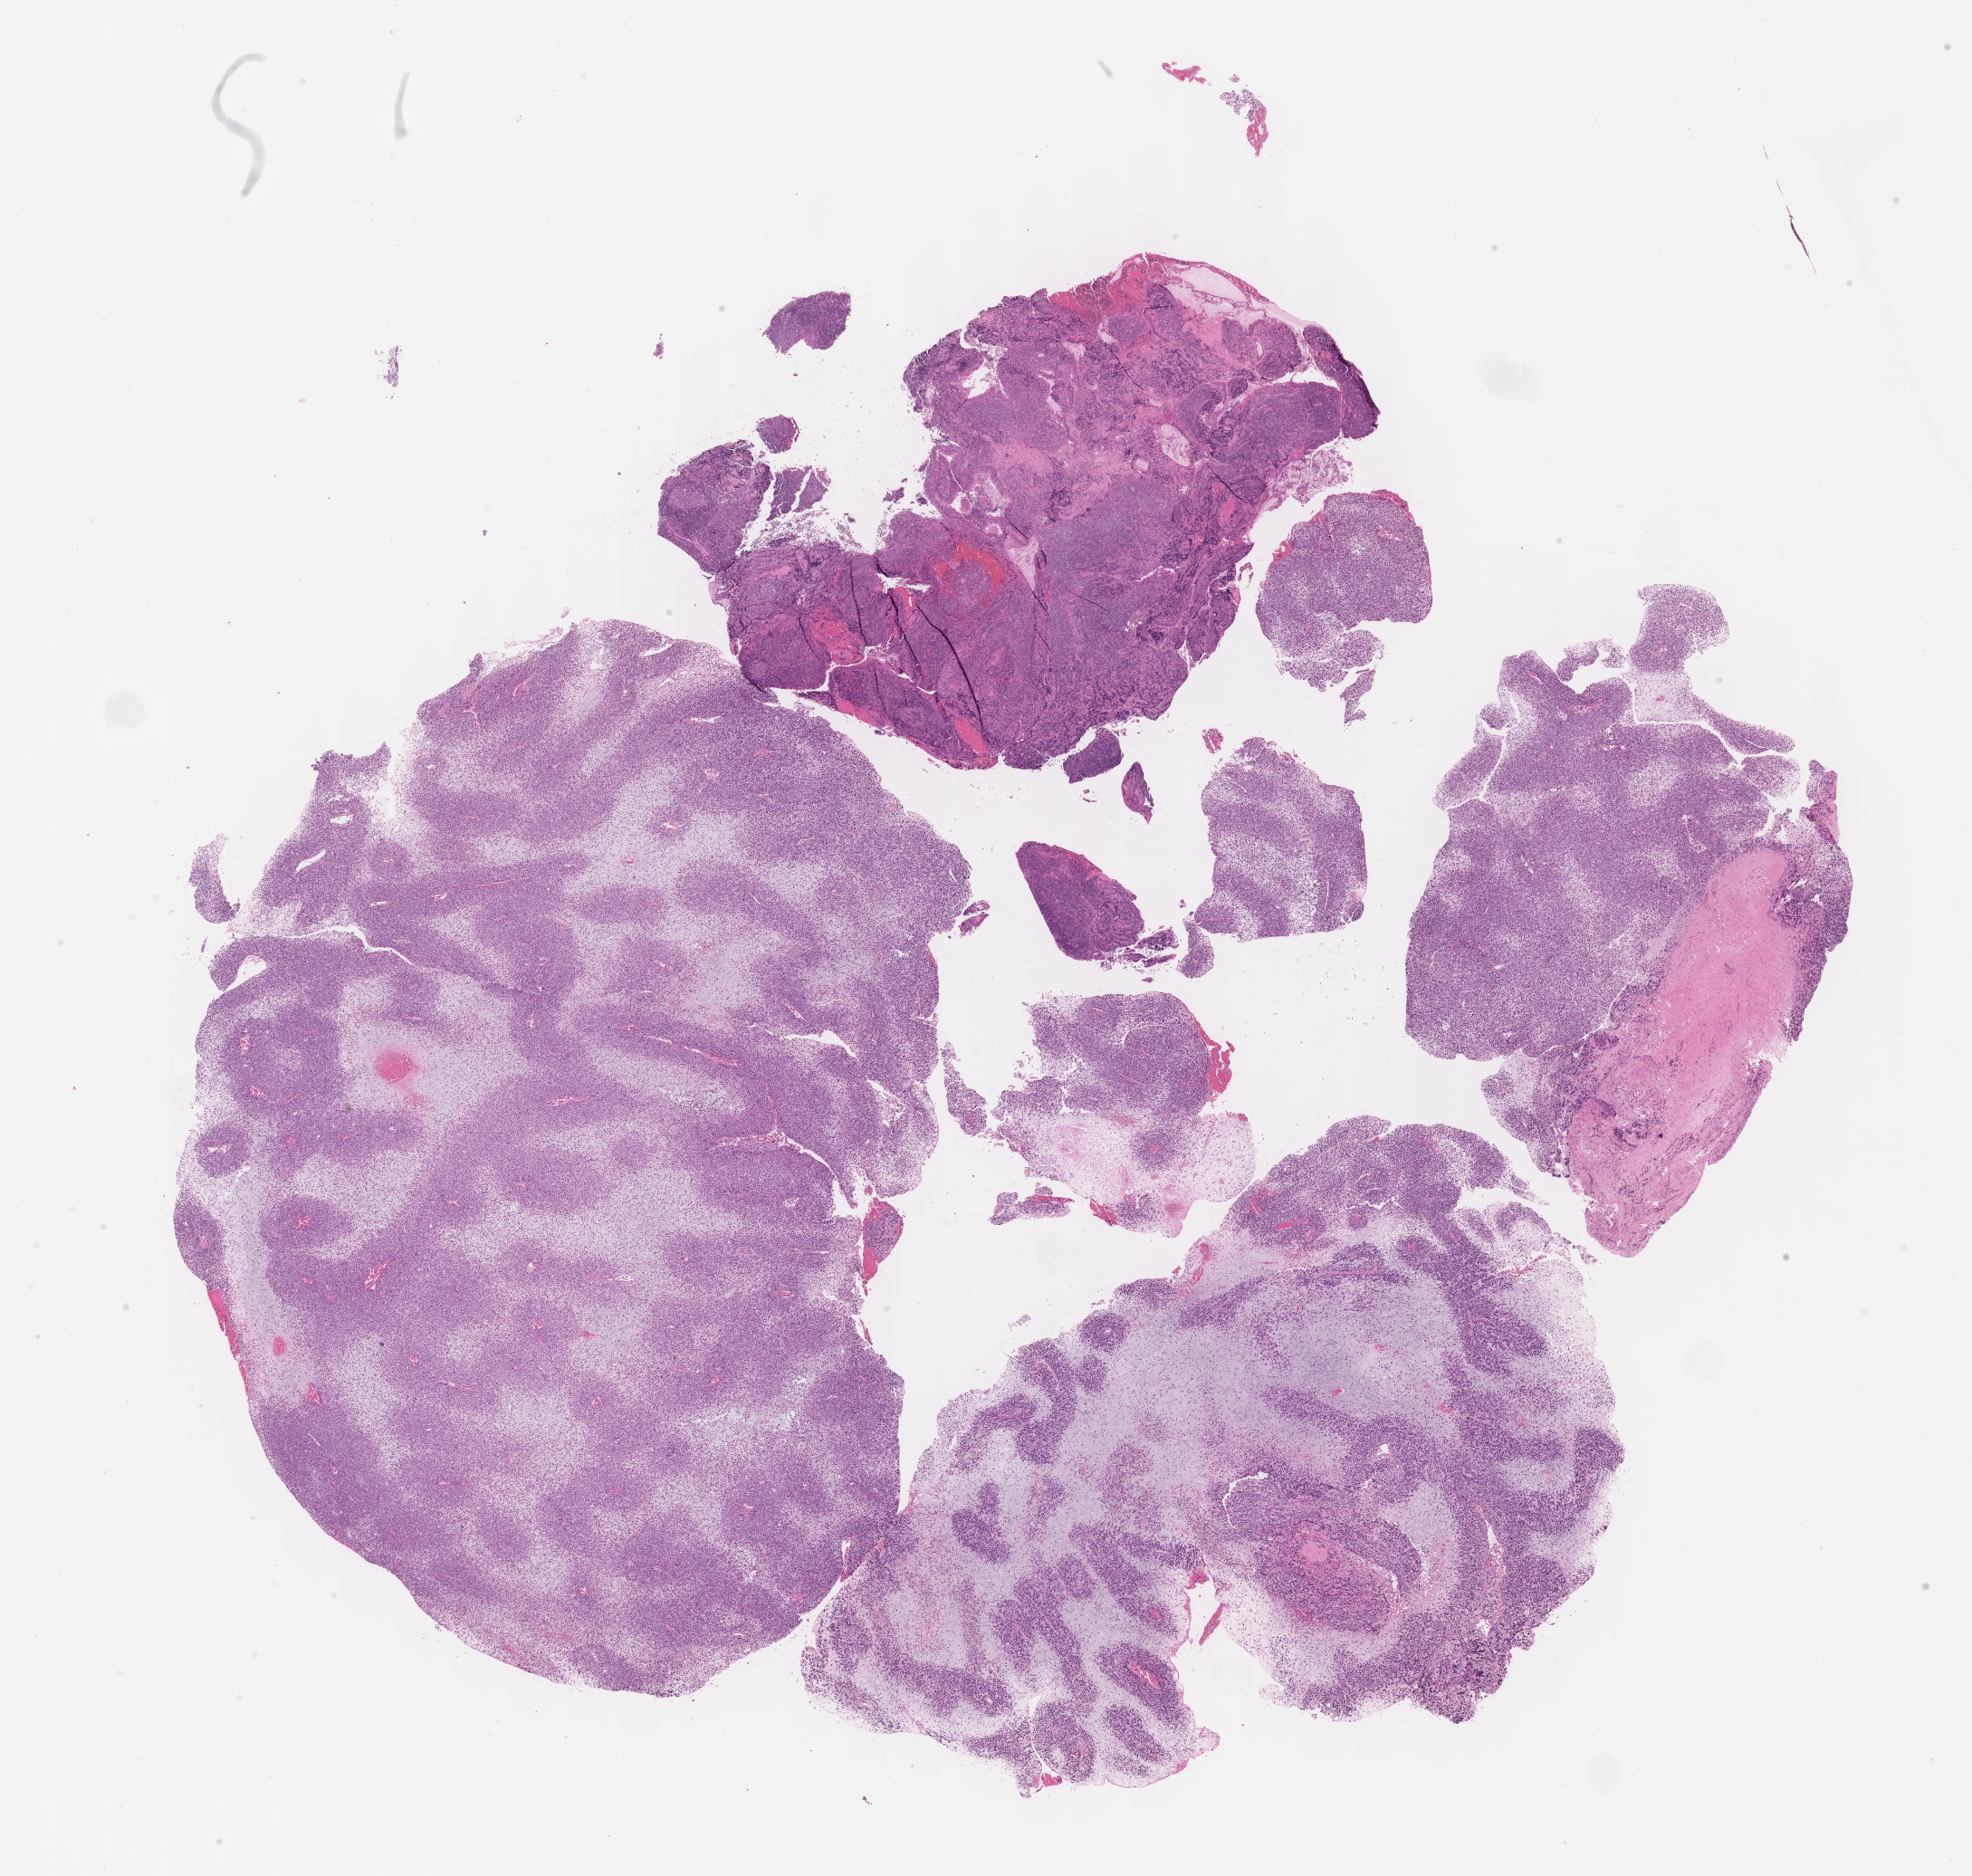
Whole-slide image, H&E stain of tumor tissue, shown as a low-resolution overview of the whole scanned area (about 17.6 x 16.8 mm); FFPE section; site: nasopharynx-left. Female patient, age at diagnosis 5.7 years.
Metastatic status at presentation (as recorded): non-metastatic. Diagnosis: rhabdomyosarcoma; histological classification: embryonal rhabdomyosarcoma. Stage (as recorded): 2.